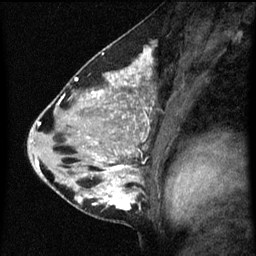
Breast MRI (dynamic contrast-enhanced), one sagittal slice; position 33 of 60 along the scan axis; dynamic contrast-enhanced series, image 2 of 3 at this slice position (ordered by acquisition); 1.5 T; TE 4.2 ms, TR 8 ms; 2.3 mm slice thickness; 256 × 256 image matrix, field of view 180 × 180 mm. Female patient, age 33 years.
Outlined on this slice (semi-automatic segmentation, software-assisted and operator-edited):
- analysis volume of interest (the breast-tissue region the enhancement analysis was run in; not a lesion): bounding box (x1, y1, x2, y2) in pixels: (71, 118, 147, 213)
- tumour enhancement mask (voxels above the 70 % enhancement threshold inside the analysis volume of interest): (78, 162, 134, 211)